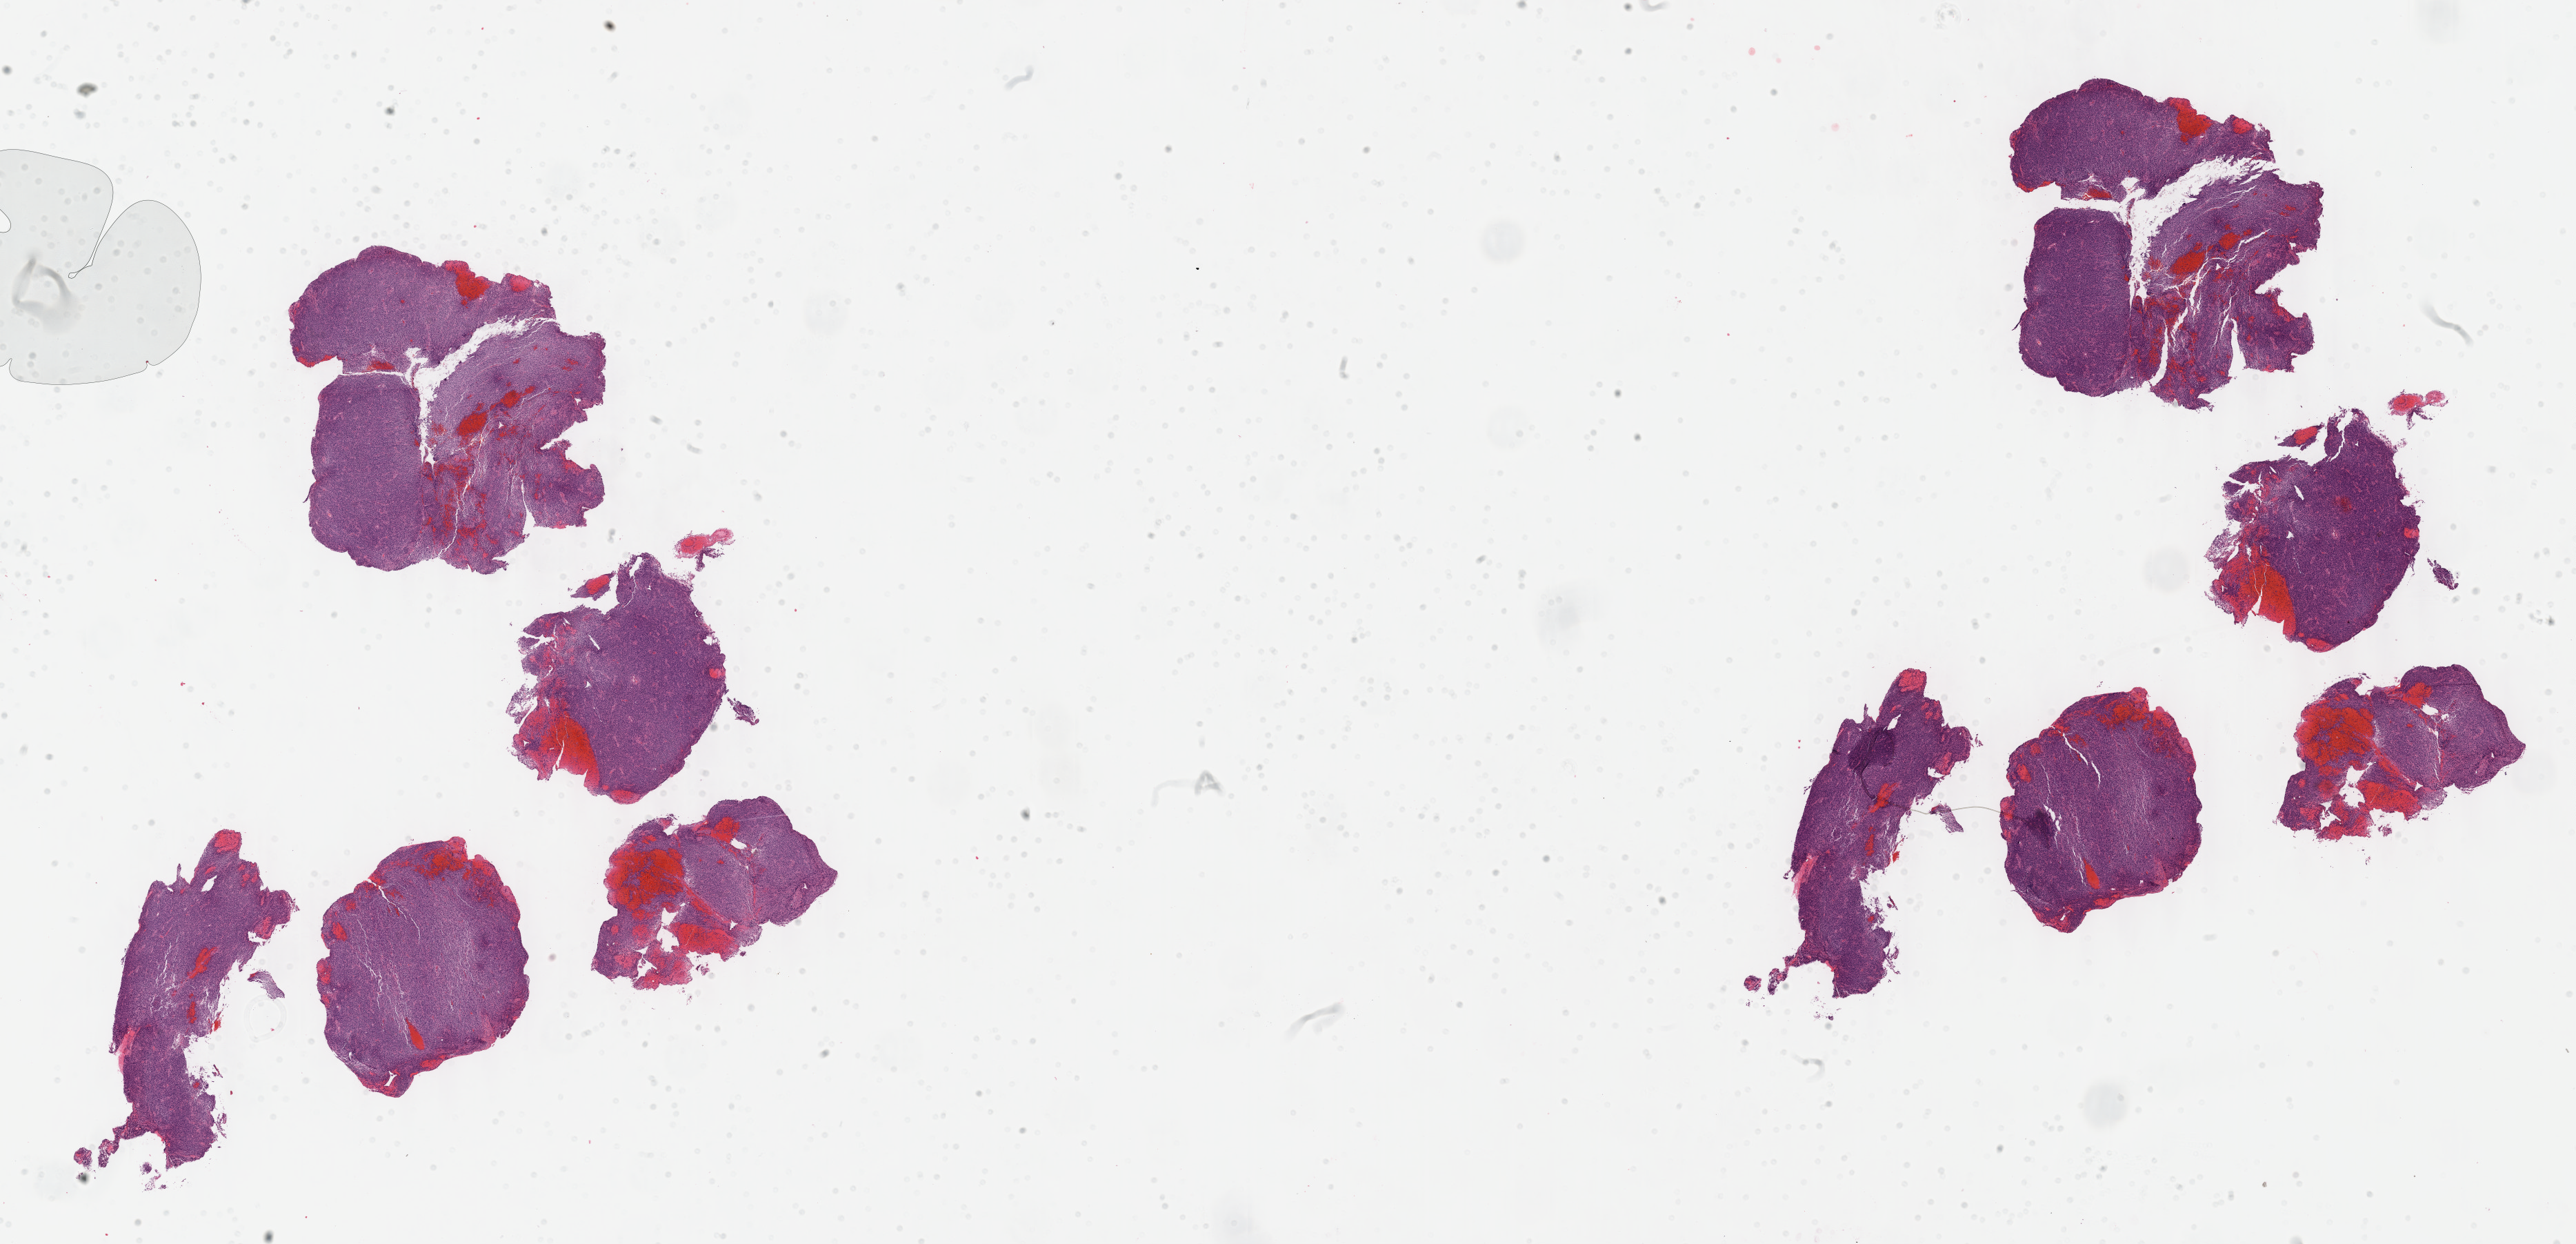
Digitized H&E tissue section (whole slide), shown as a low-resolution overview of the whole scanned area (about 30.2 x 14.6 mm, acquisition: 40x scan), formalin-fixed paraffin-embedded (FFPE) diagnostic section, primary tumour sample from the brain. Male patient; age at initial diagnosis 30 years. Histologic grade: G3 (poorly differentiated).
Laterality: left. Pathologic diagnosis: Oligodendroglioma, anaplastic (cerebrum).